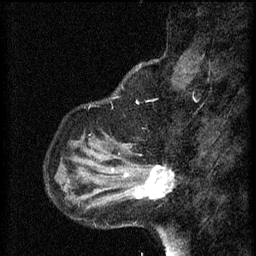
Breast MRI (dynamic contrast-enhanced), one sagittal slice. Slice 14 of 60 in the series (ordered by position). 3 images stored at this slice position (order not interpretable as contrast timing). 1.5 T. TE 4.2 ms, TR 8.2 ms. 256 × 256 image matrix. Female patient, age 37 years.
Outlined on this slice (semi-automatic segmentation, software-assisted and operator-edited):
- analysis volume of interest (the breast-tissue region the enhancement analysis was run in; not a lesion): bounding box <126,156,175,205> (left, top, right, bottom; pixels)
- tumour enhancement mask (voxels above the 70 % enhancement threshold inside the analysis volume of interest): <126,166,174,199>